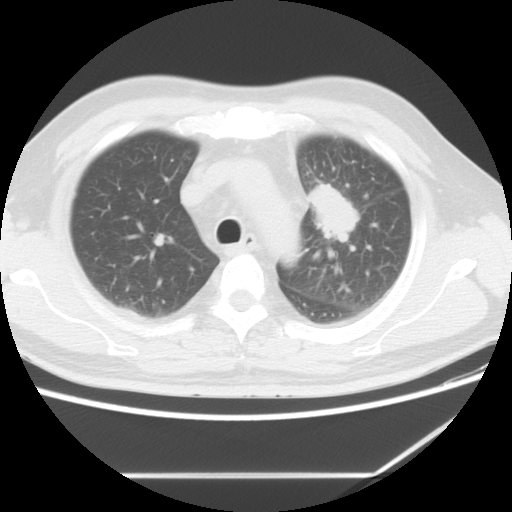
Chest CT, one axial slice; slice 6 of 10 in the series (ordered by position); 120 kVp; lung window (W 1500 / L -600 HU); 5 mm slice thickness; 512 × 512 image matrix, field of view 350 × 350 mm. Male patient, age 56 years. Case-level facts recorded for this patient, not image findings: clinical TNM (as recorded): T2 N3 M1.
Structures marked on this image (rectangle marked by the reading radiologist):
- lung tumour (recorded histology: adenocarcinoma): bounding box <304,171,361,248> (left, top, right, bottom; pixels)